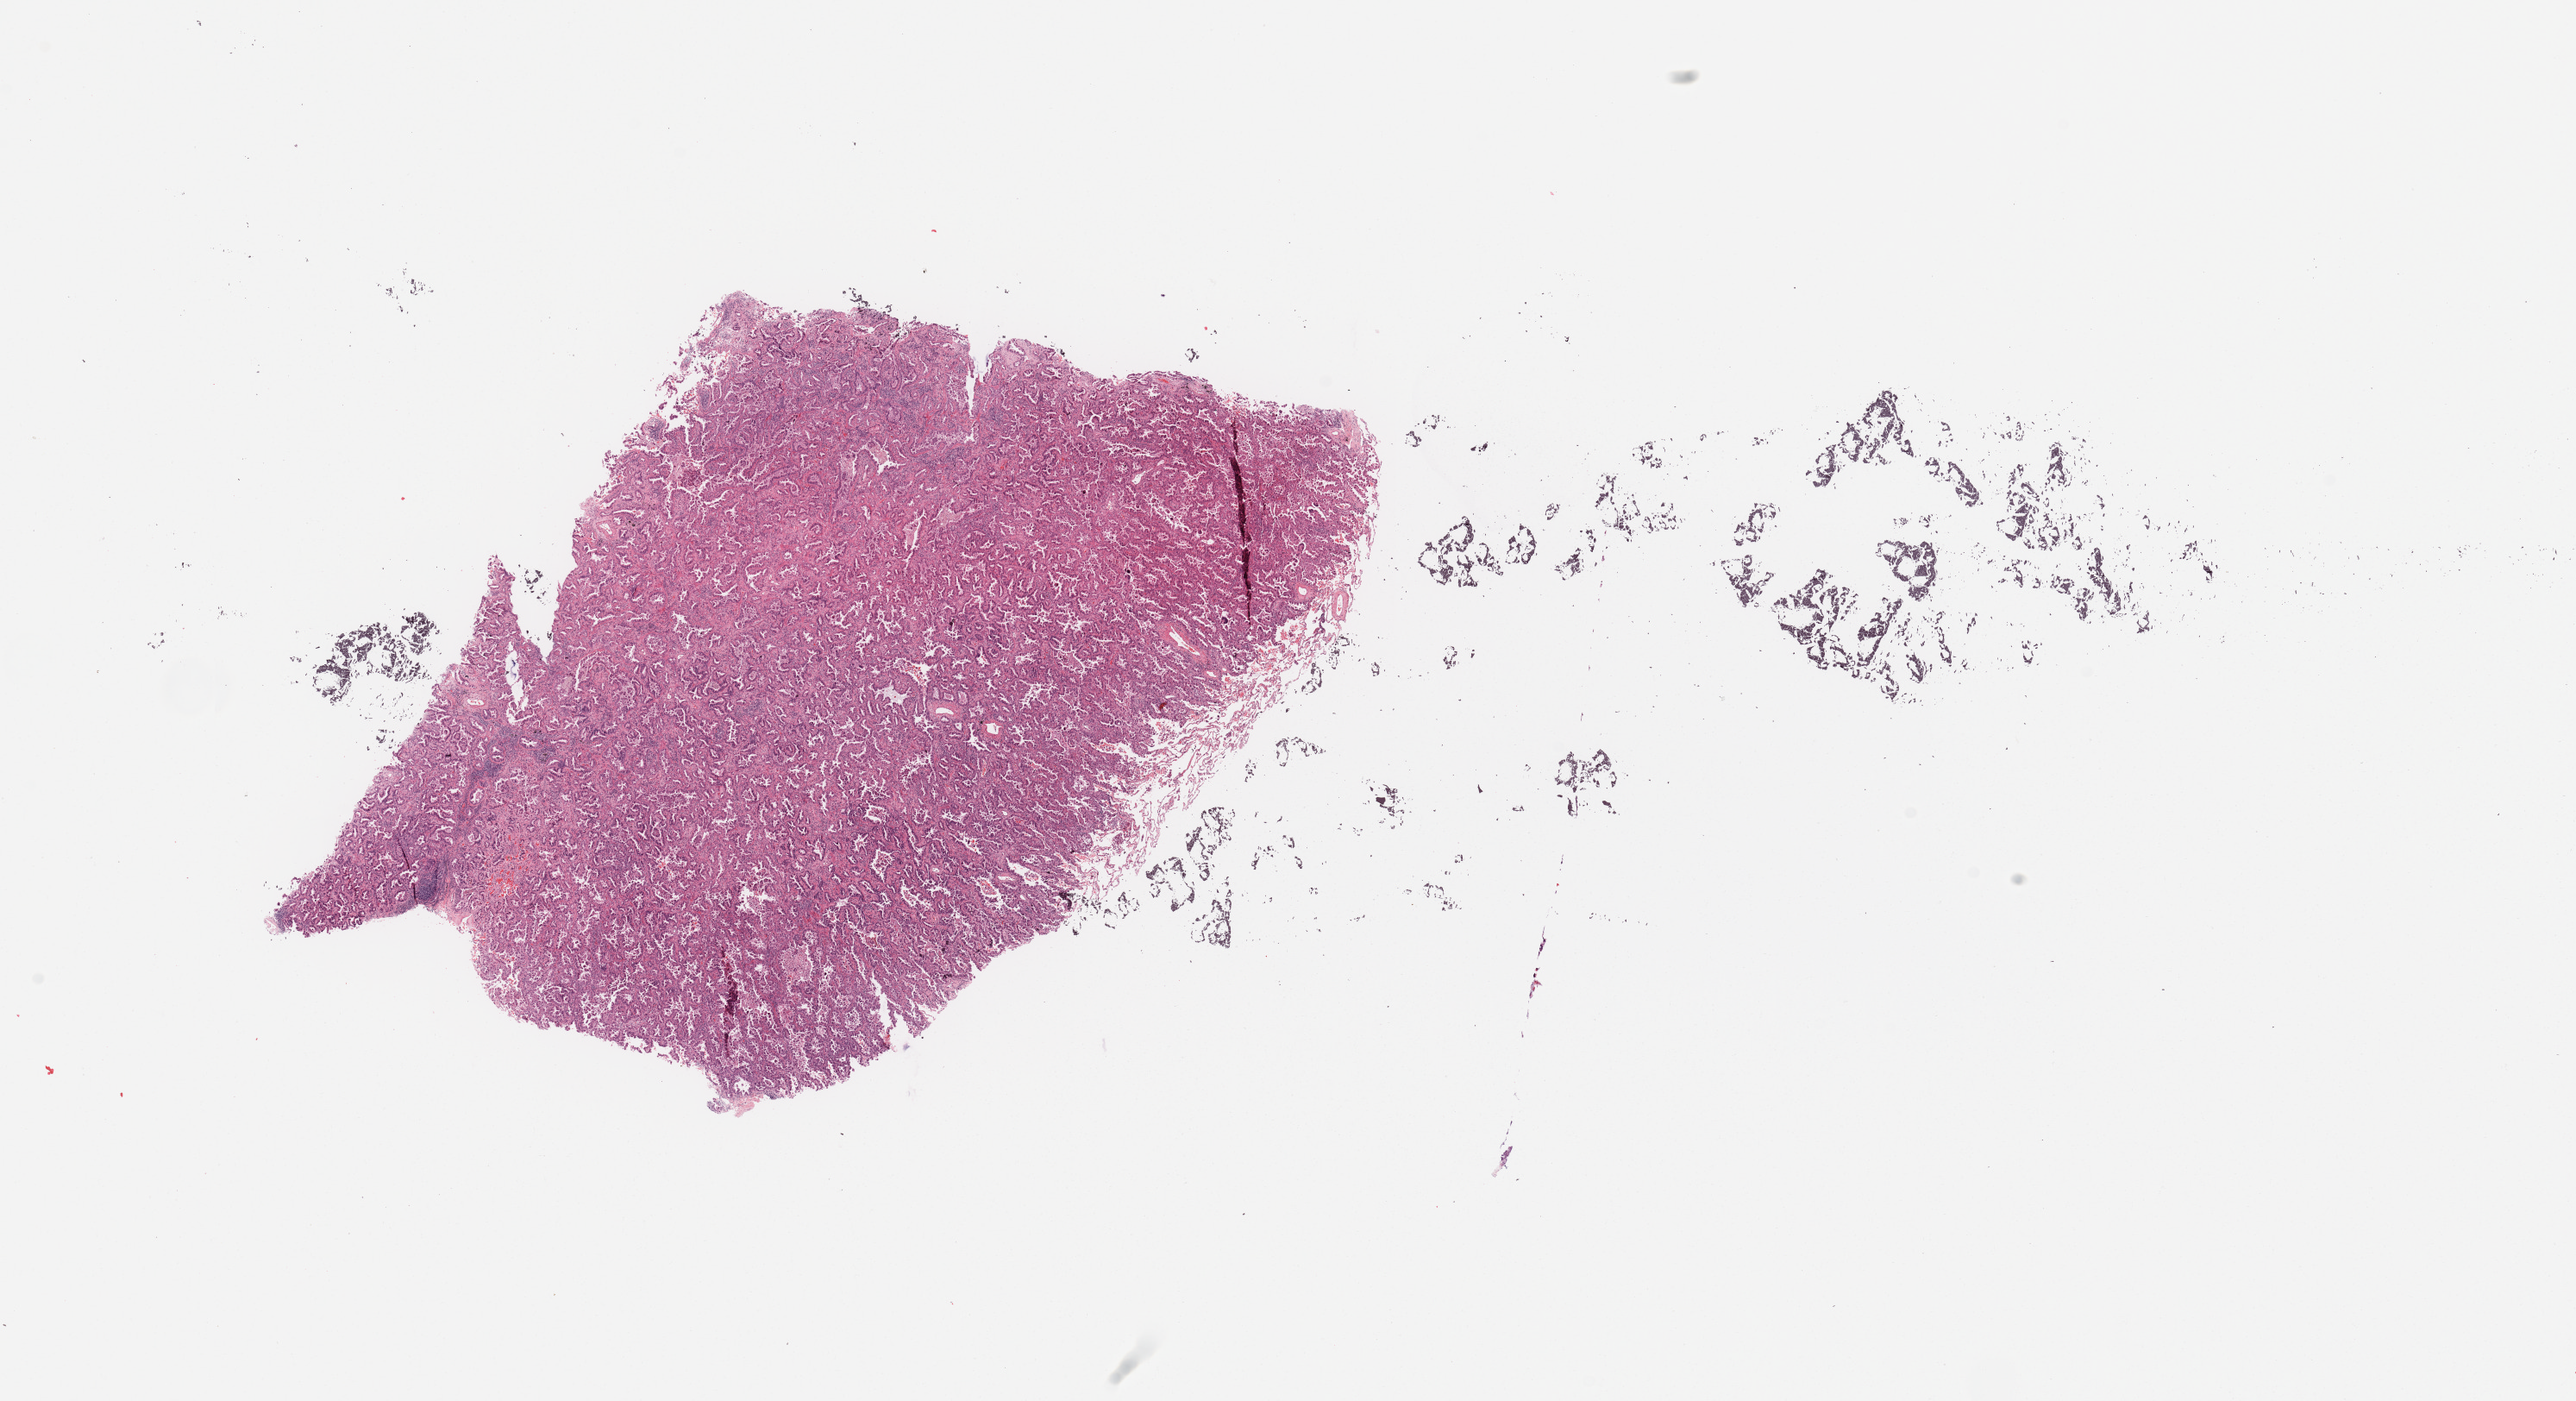
H&E-stained whole-slide image, whole scanned area (about 23.6 x 12.8 mm, from a 20x scan) shown as a low-resolution overview, tumour tissue sample, sampled site: lung. Female, 76 y/o. Histologic grade: G2 (moderately differentiated). Composition of this section per pathologist review: tumour nuclei 80%, necrosis 3%.
Histologic diagnosis: Adenocarcinoma, NOS. Primary tumour site (as recorded): right lower lobe. AJCC pathologic stage: IIIA.